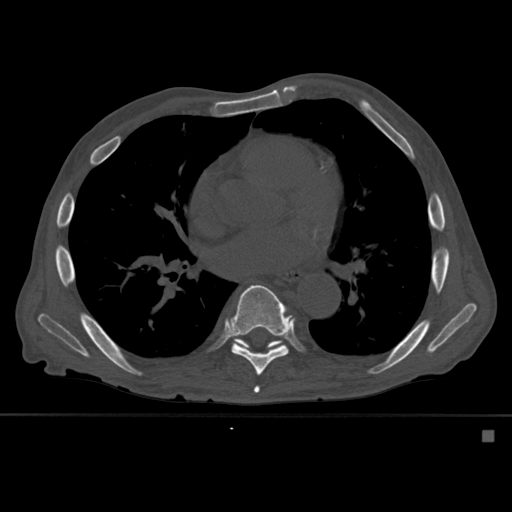
CT including the spine, one axial slice; position 348 of 527 along the scan axis; bone window (W 1800 / L 400 HU); 1.5 mm slice thickness; 512 × 512 image matrix, field of view 373 × 373 mm. Male patient, age 78 years. Case-level facts recorded for this patient, not image findings: primary cancer: prostate.
Outlined on this slice (semi-automatic segmentation, software-assisted and operator-edited):
- T7 vertebra: bounding box <254,386,260,393> (left, top, right, bottom; pixels)
- T8 vertebra: <228,284,294,376>
- T9 vertebra: <231,336,285,350>